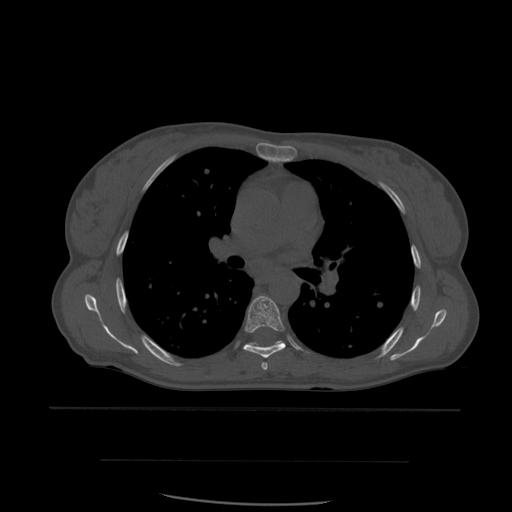
CT including the spine, one axial slice; slice 391 of 574 in the series (ordered by position); bone window (W 1800 / L 400 HU); 1.25 mm slice thickness; 512 × 512 image matrix, field of view 392 × 392 mm. Patient age 48 years. Case-level facts recorded for this patient, not image findings: primary cancer: lung; vertebrae with lytic lesions (as recorded): T11.
Outlined on this slice (semi-automatic segmentation, software-assisted and operator-edited):
- T5 vertebra: bounding box [x1, y1, x2, y2] px = [262, 362, 268, 370]
- T6 vertebra: [243, 296, 286, 359]
- T7 vertebra: [247, 341, 285, 347]